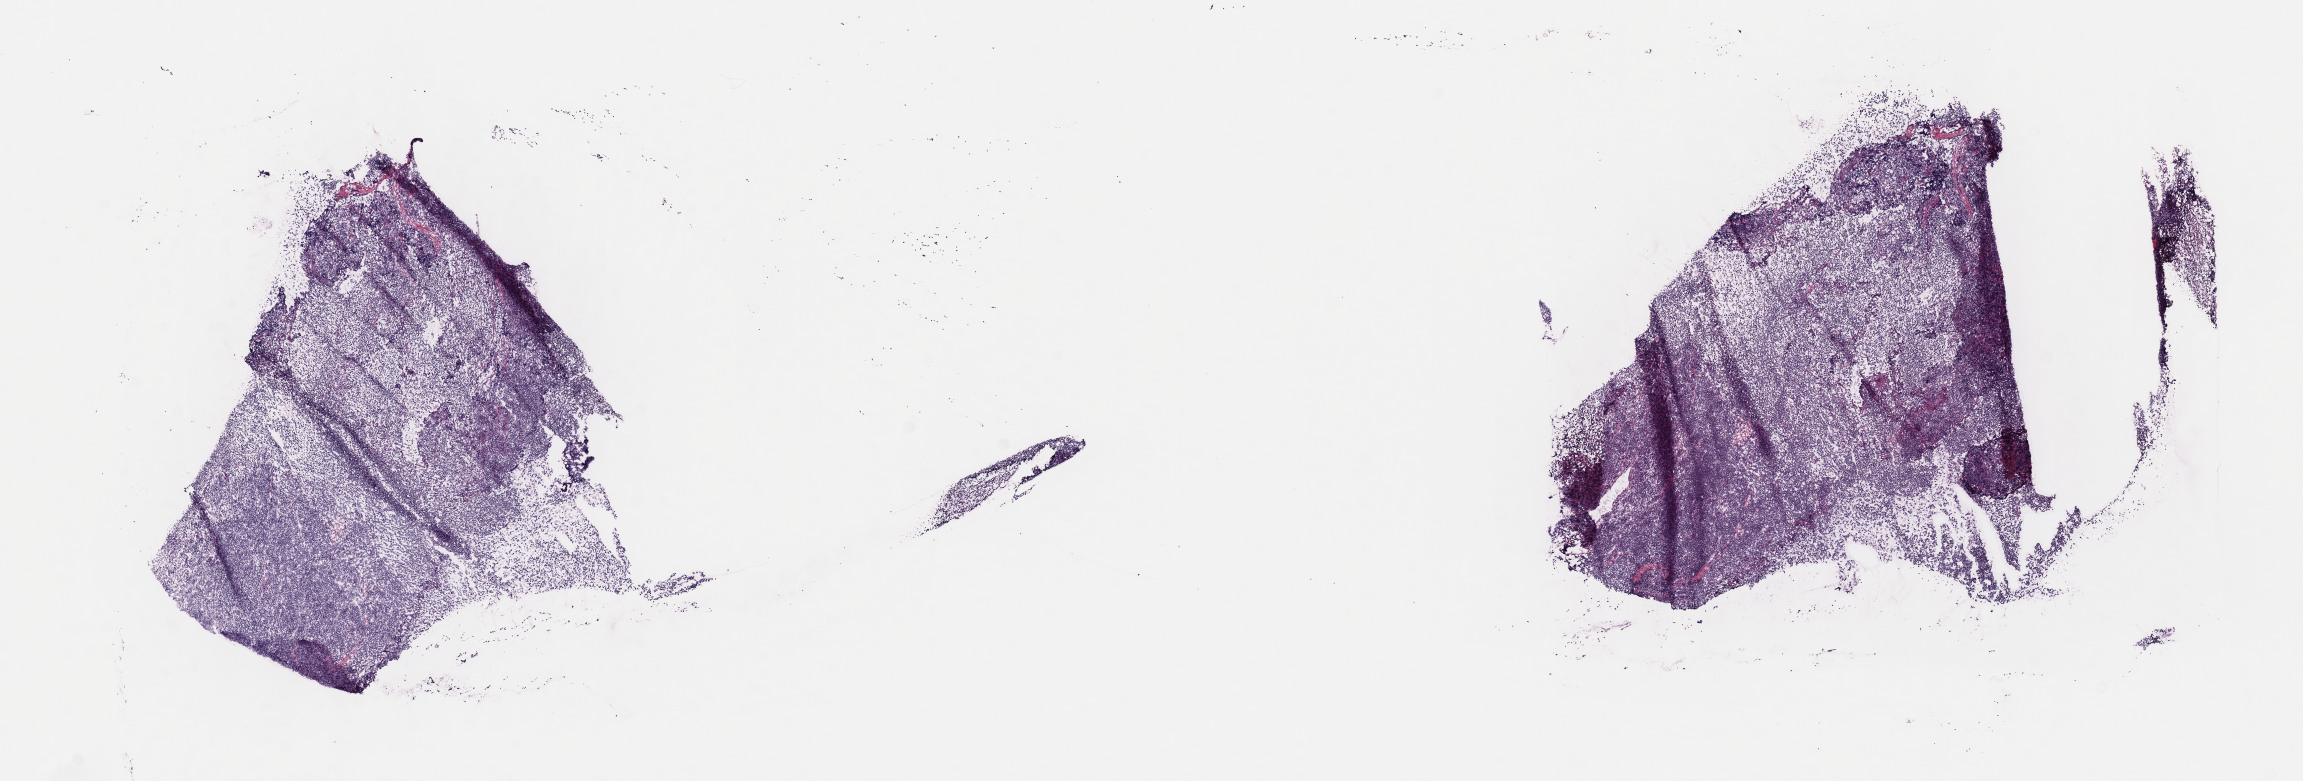
Haematoxylin and eosin whole-slide image, low-resolution overview of the scanned area, about 18.6 x 6.3 mm. Frozen section (tissue freezing medium). Specimen: primary tumor. Anatomic site: mandible. Male, age 4 years at initial diagnosis. Composition of this section per pathologist review: tumor cells 93%, tumor nuclei 90%, stromal cells 5%, necrosis 2%, normal cells 0%. Infiltration values recorded for this section: lymphocyte infiltration 3%, monocyte infiltration 3%, neutrophil infiltration 0%.
Ann Arbor stage (patient): Stage I. Histologic diagnosis: Burkitt lymphoma, NOS.